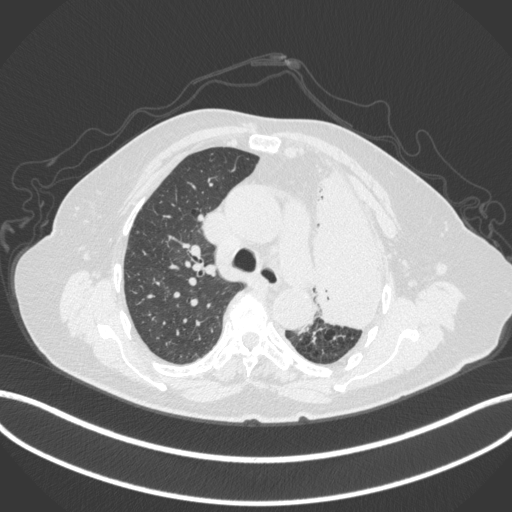
Chest CT, one axial slice. Position 269 of 399 along the scan axis. Reconstruction kernel B31f. Lung window (W 1500 / L -600 HU). 512 × 512 image matrix. Patient: female, 75 years. Case-level facts recorded for this patient, not image findings: clinical TNM (as recorded): T3 N3 M1.
Structures marked on this image (bounding box drawn by a radiologist):
- lung tumour (recorded histology: adenocarcinoma): bounding box [x1, y1, x2, y2] px = [315, 159, 393, 334]